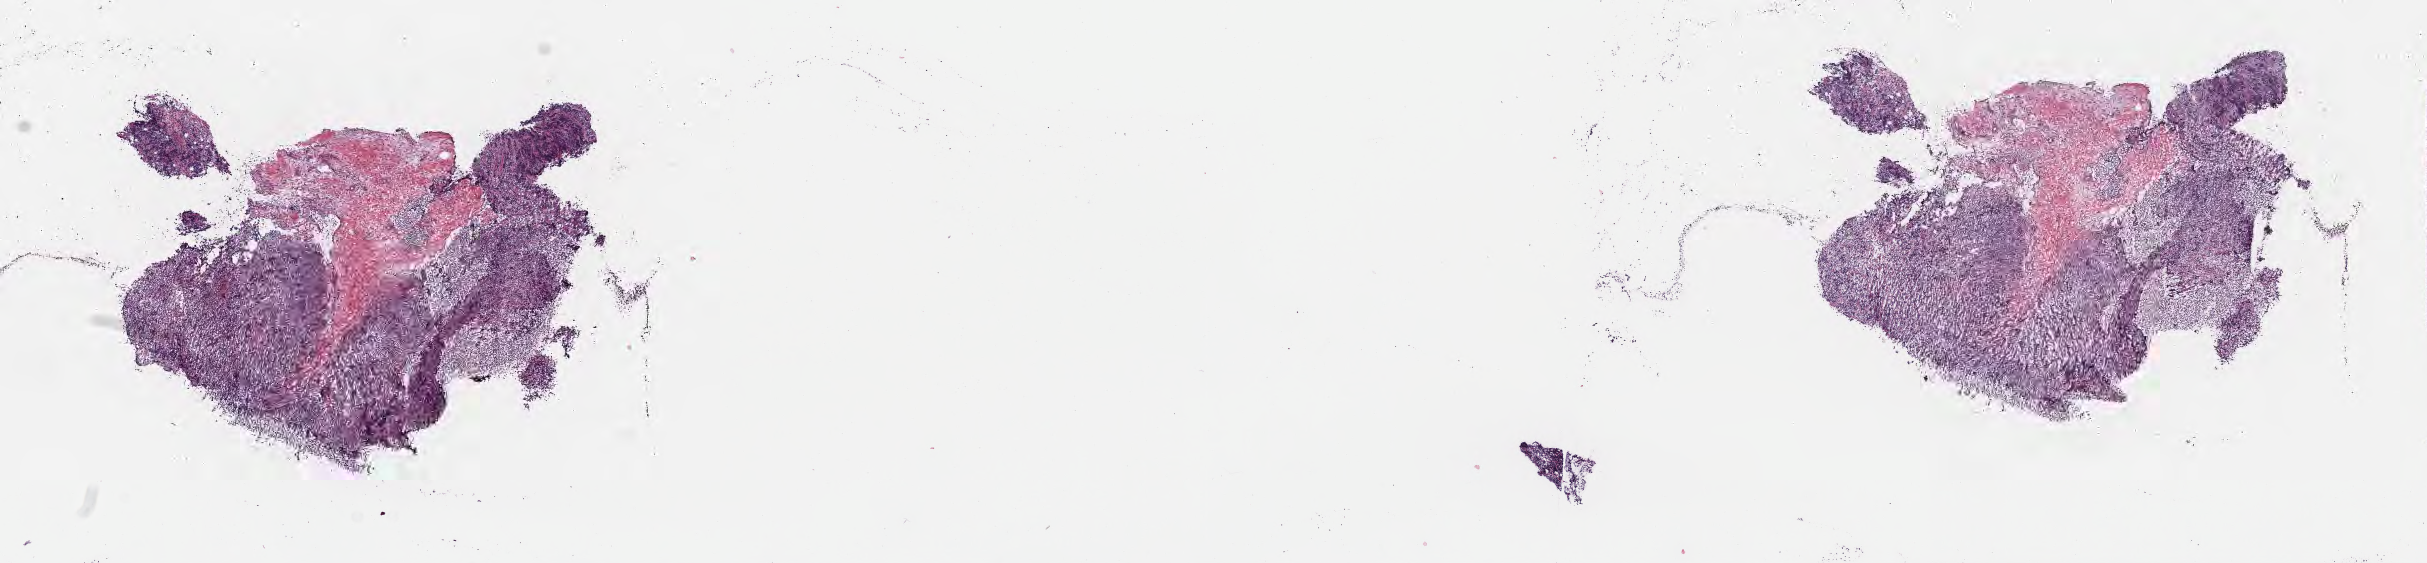
Digitized H&E-stained section, shown as a low-resolution overview of the whole scanned area (about 19.6 x 4.6 mm), cryosection, specimen: primary tumor, anatomic site: mandible. Patient: female, aged 13. Slide review estimates, as recorded: tumor cells 65%, tumor nuclei 90%, stromal cells 30%, necrosis 5%, normal cells 0%. Inflammatory infiltration, as recorded: lymphocyte infiltration 60%, monocyte infiltration 25%, neutrophil infiltration 5%.
Diagnosis: Burkitt lymphoma, NOS. Ann Arbor stage (patient): Stage III. Section: top of the tissue portion.